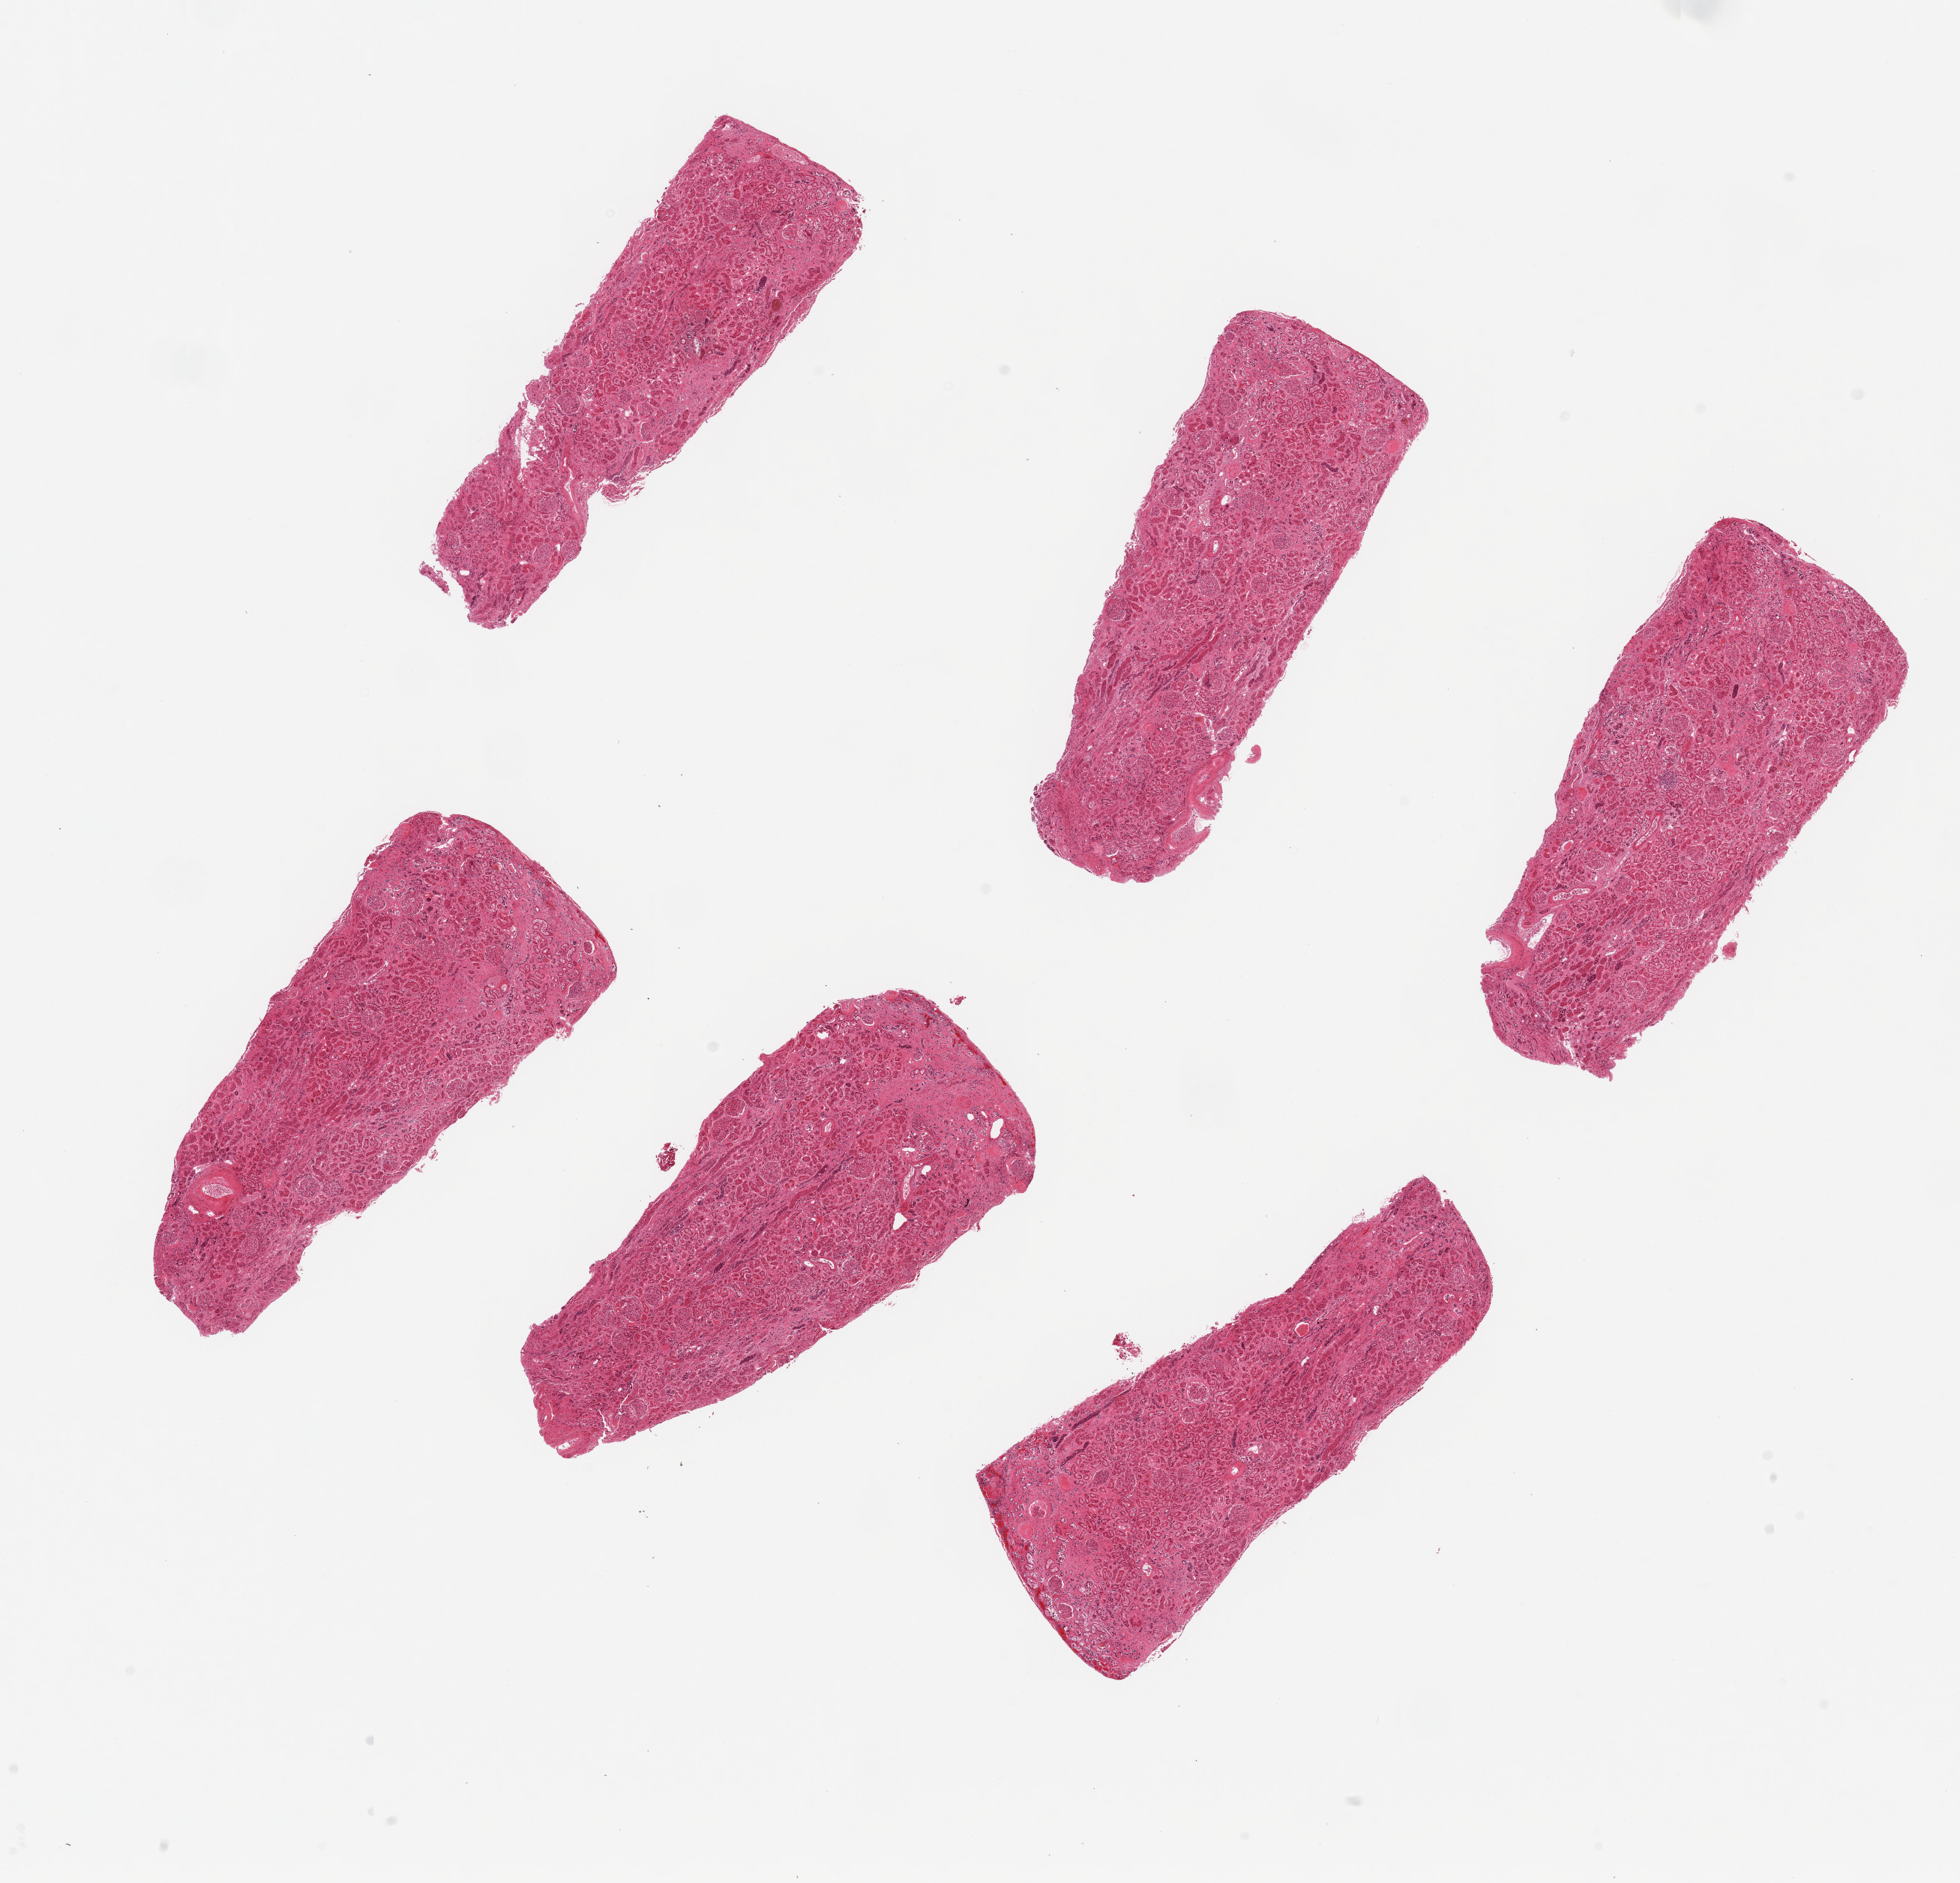
Whole-slide image, hematoxylin and eosin (H&E) stain, a low-resolution overview of the entire scanned area, about 20.7 x 19.9 mm (from a 20x scan), PAXgene-fixed paraffin-embedded (PFPE) section, sampled site (target tissue): renal cortex, donor tissue sample. Male donor.
Reviewer comment on this tissue sample: 6 pieces; arterio and arteriolonephrosclerosis, interstitial fibrosis with scarring, autolysis/cannot distinguish from acute tubular necrosis.